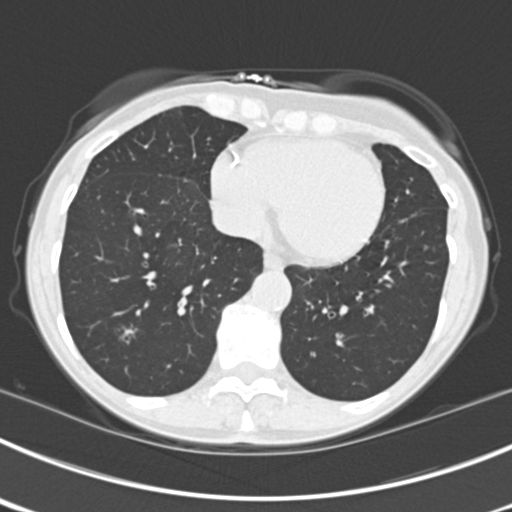
Chest CT (low-dose screening protocol), one axial image; third screening round (two years after baseline); lung window (W 1500 / L -600 HU); 2 mm slice thickness; standard (soft-tissue) reconstruction kernel (B30f); 120 kVp; 512 × 512 image matrix, field of view 302 × 302 mm. Female participant, aged 63 years at enrolment.
Expert-annotated lung lesion, bounding box [x1, y1, x2, y2] px = [104, 312, 149, 359]. The screening reader recorded 9 non-calcified nodules or masses ≥4 mm on this exam; which of them this box marks is not recorded. Official screen result: positive, other. Later outcome: lung cancer diagnosed 15 days after this screen — bronchiolo-alveolar adenocarcinoma, NOS, right upper lobe, right middle lobe, right lower lobe, left upper lobe, left lower lobe, moderately differentiated (G2), stage IV (AJCC 6th edition).